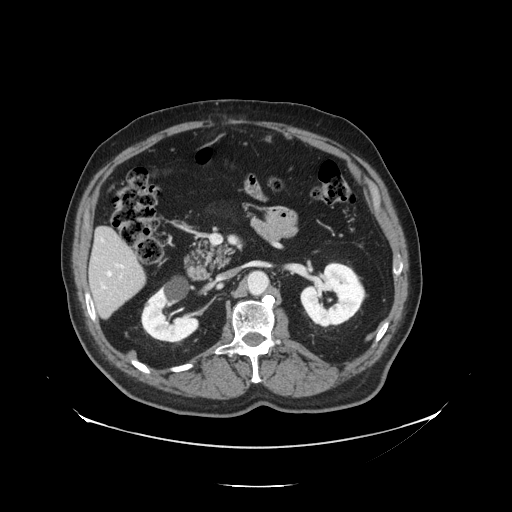
Contrast-enhanced abdominal CT, one axial slice. Slice 59 of 138 in the series (ordered by position). Intravenous contrast given. Soft-tissue window (W 400 / L 40 HU). 2.5 mm slice thickness. 512 × 512 image matrix, field of view 497 × 497 mm. Male patient, age 77 years. Case-level facts recorded for this patient, not image findings: diagnosis: colorectal cancer liver metastases, imaged before liver resection; multiple liver metastases: no; largest metastasis: 1.5 cm; disease in both lobes: no.
Annotated regions visible in this slice (outlined manually by an expert reader):
- liver: box from (x=91, y=229) to (x=145, y=317) px
- planned liver remnant (the part of the liver to remain after resection): (x=92, y=229)–(x=141, y=284)